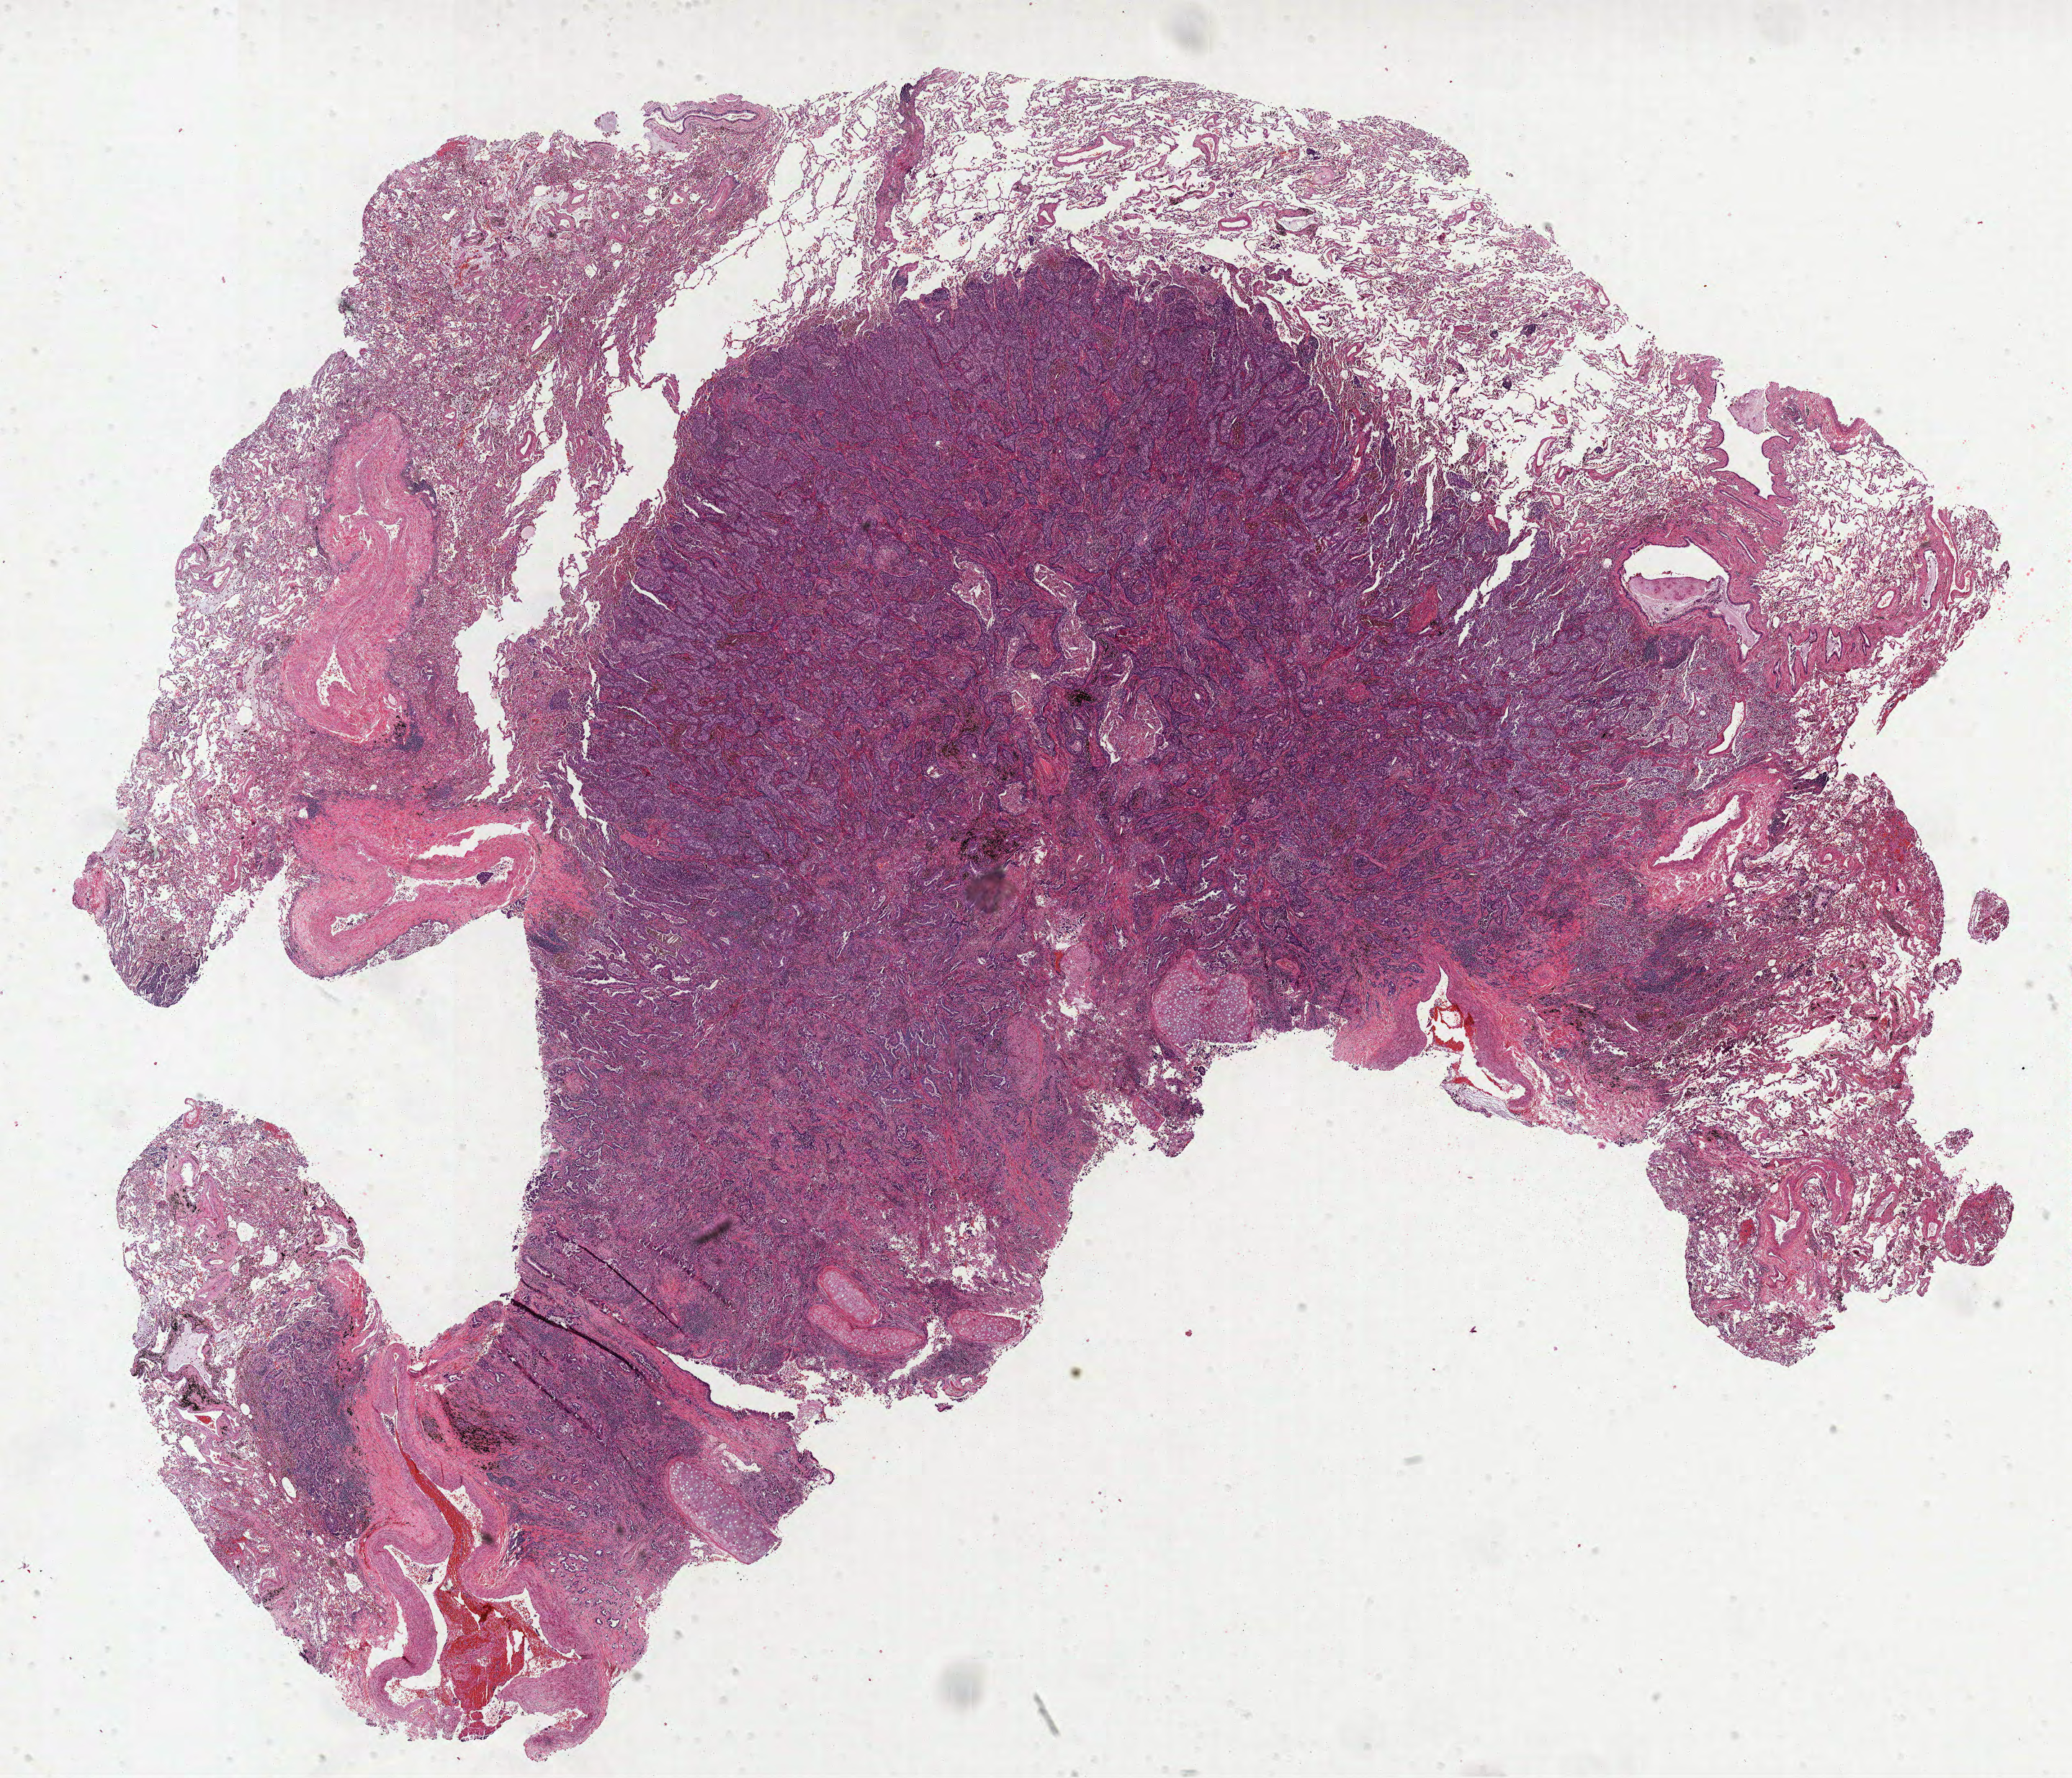
Hematoxylin and eosin (H&E) stained whole-slide image, shown as a low-resolution overview of the whole scanned area (about 23.2 x 19.9 mm), formalin-fixed paraffin-embedded (FFPE) diagnostic section, lung, primary tumour sample. Male patient; age at initial diagnosis 60 years.
- laterality: right
- pathologic diagnosis: Adenocarcinoma, NOS (lower lobe, lung)
- AJCC pathologic stage: IA (7th edition)